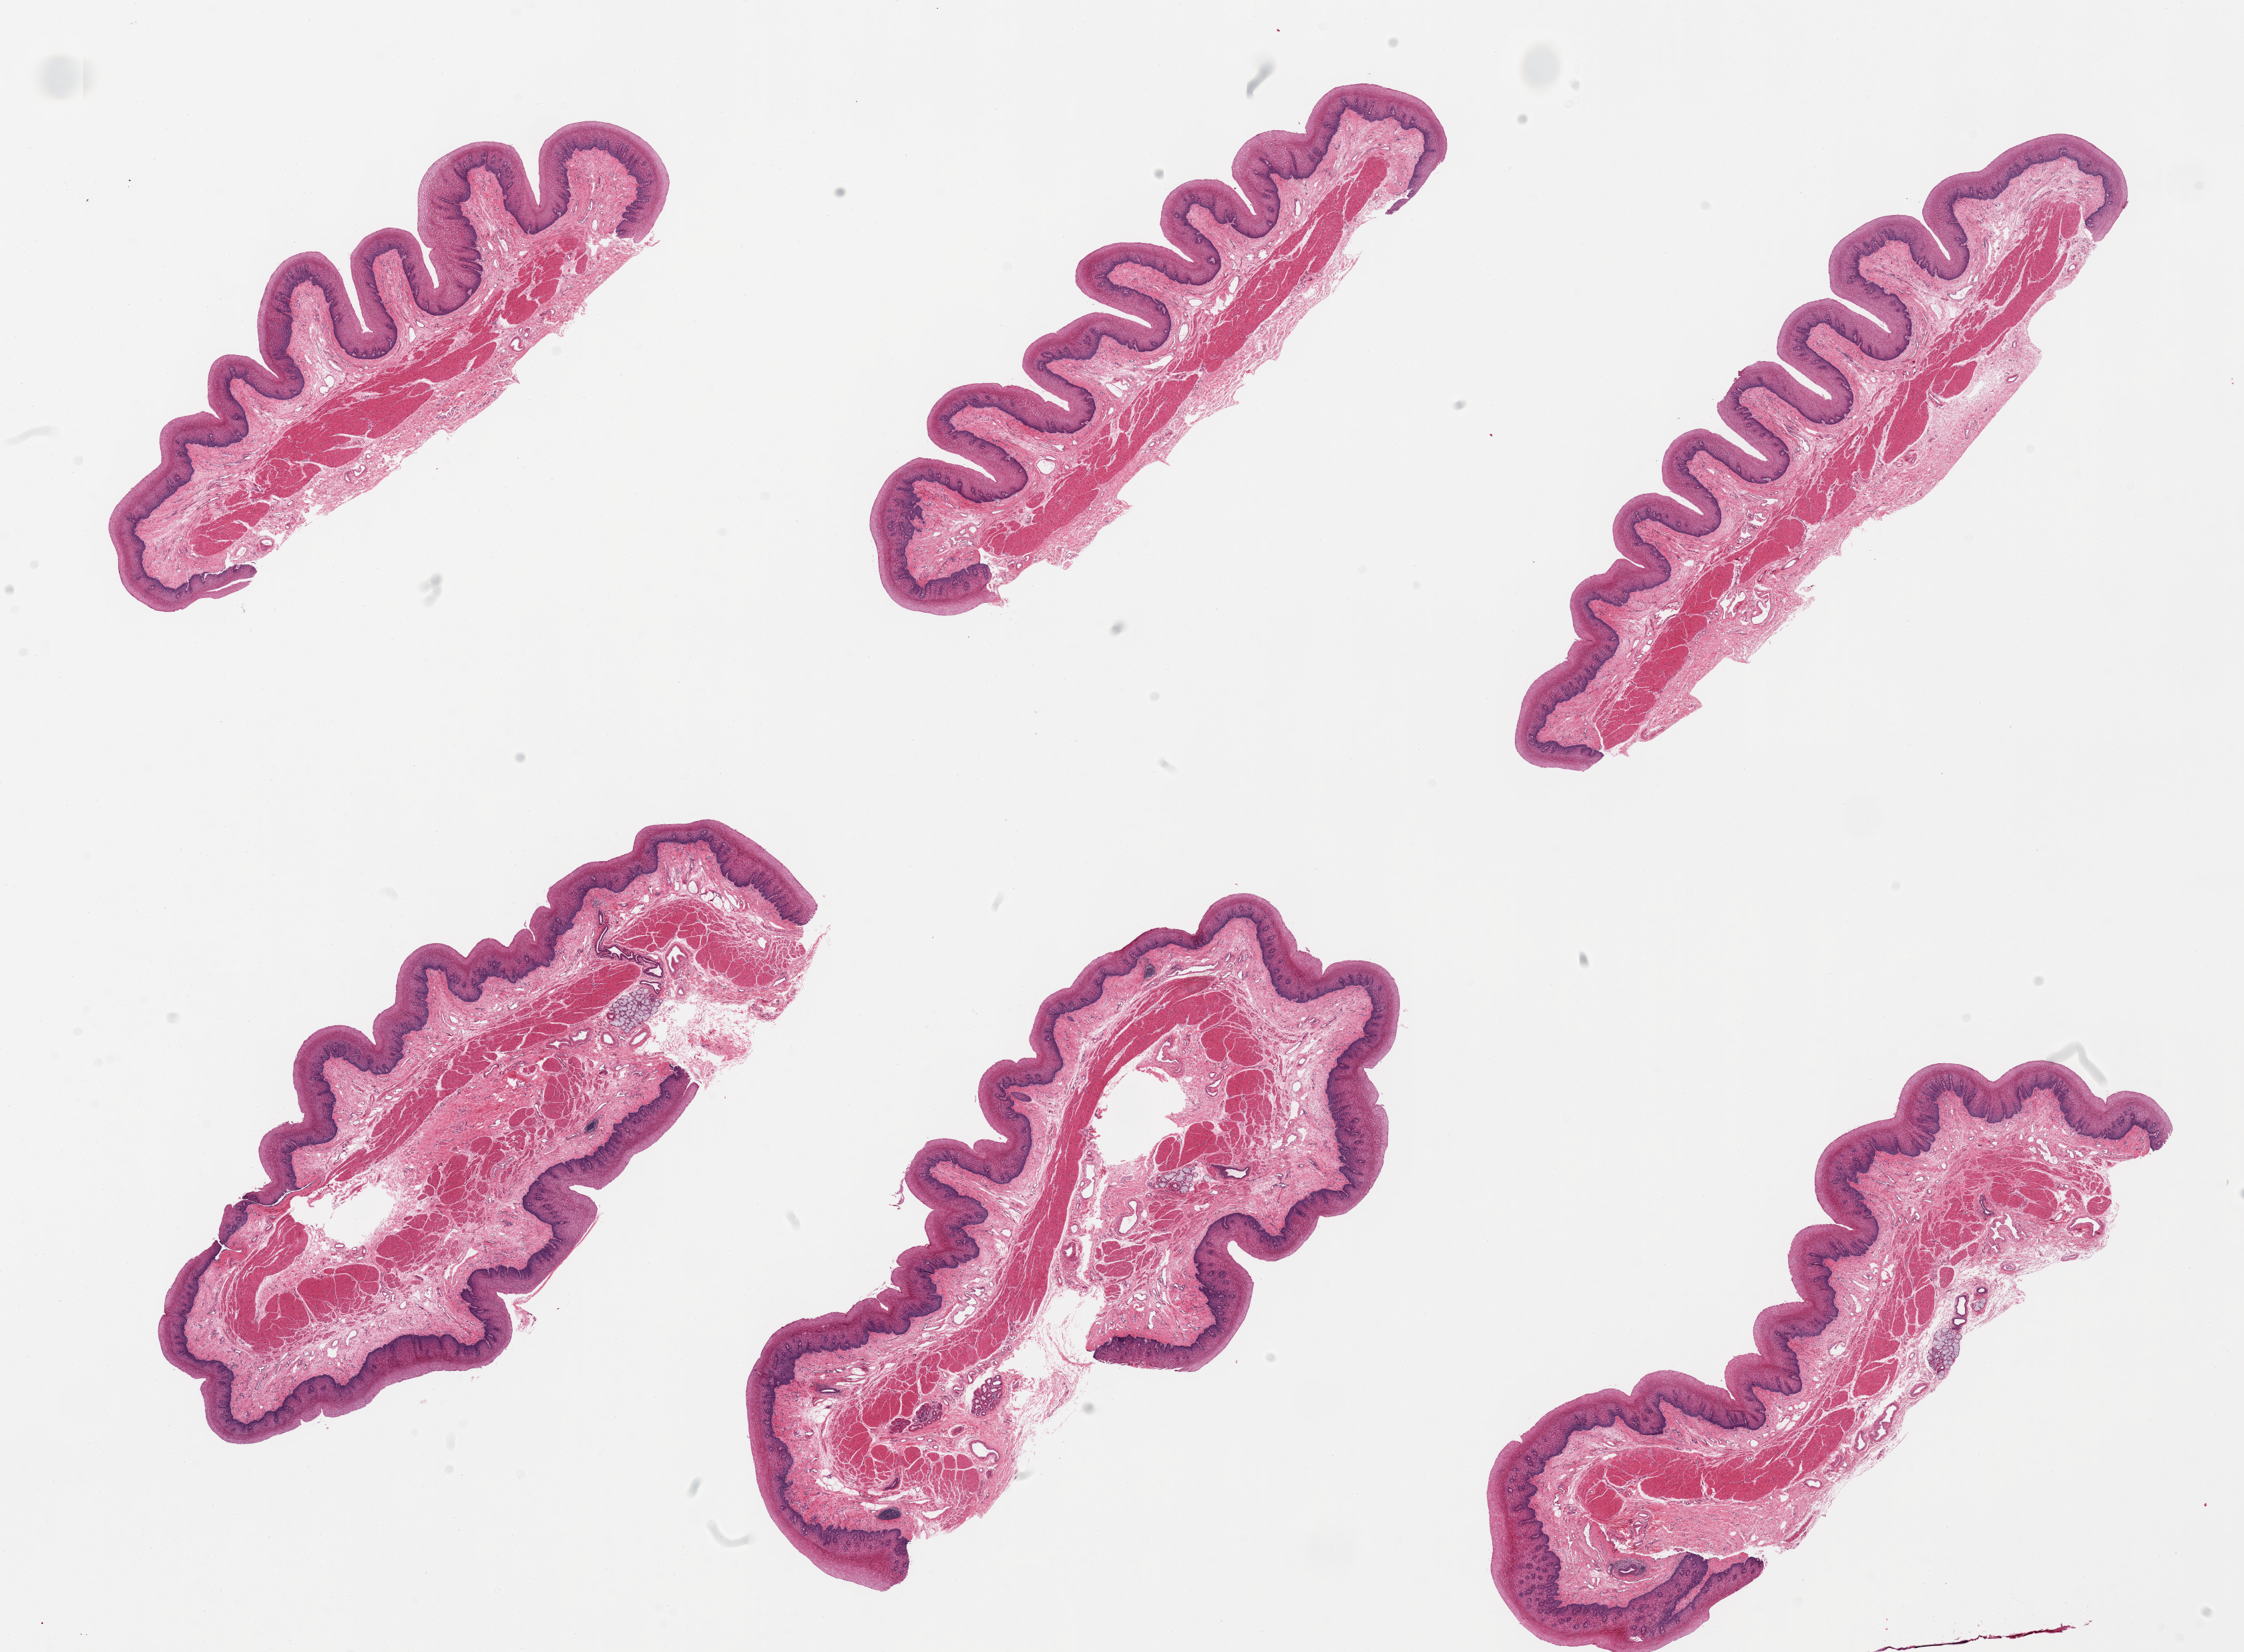
Whole-slide image, hematoxylin and eosin (H&E) stain — low-resolution overview of the scanned area, about 26.6 x 19.6 mm (slide scanned at 20x); PAXgene-fixed paraffin-embedded (PFPE) section; sampled site (target tissue): esophageal mucous membrane; tissue donor sample.
Pathologist's review note for this sample: 6 pieces, well trimmed of muscularis, few submucosal glands (some).